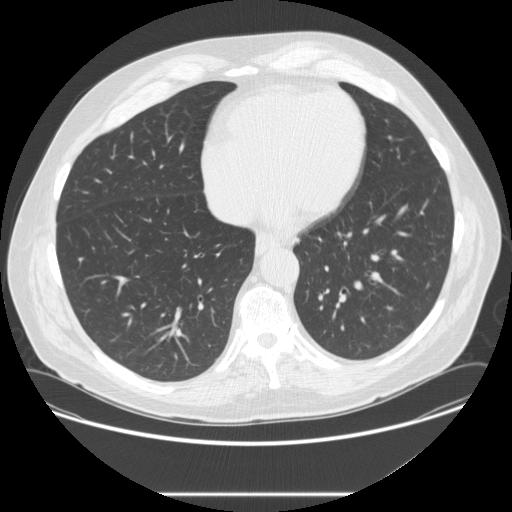
Low-dose screening chest CT, axial slice. Second screening round (one year after baseline). Lung window (W 1500 / L -600 HU). 2.5 mm slice thickness. Standard (soft-tissue) reconstruction kernel (STANDARD). Slice 174 of 262 in the series. Male, age 67 years at enrolment. Current smoker at enrolment.
• Lesion marked by an expert reader, bounding box (x1, y1, x2, y2) in pixels: (417, 276, 442, 301).
• Screening reader's record for this exam (one nodule recorded; not confirmed to be the boxed lesion): non-calcified nodule or mass ≥4 mm, left lower lobe, 4 × 4 mm, poorly defined margins, soft tissue attenuation, pre-existing on the prior screen: yes; interval growth: no.
• Official screen result: positive, other.